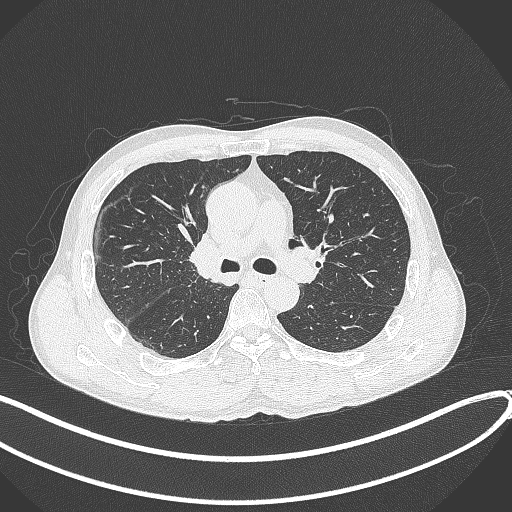
Chest CT, one axial slice. Slice 238 of 409 in the series (ordered by position). Reconstruction kernel B70f. Lung window (W 1500 / L -600 HU). 512 × 512 image matrix, field of view 400 × 400 mm. Male patient, age 53 years. From the clinical record (not read from this slice): clinical TNM (as recorded): T1b N0 M0.
Structures marked on this image (bounding box drawn by a radiologist):
- lung tumour (recorded histology: squamous cell carcinoma): bounding box [x1, y1, x2, y2] px = [185, 231, 222, 286]